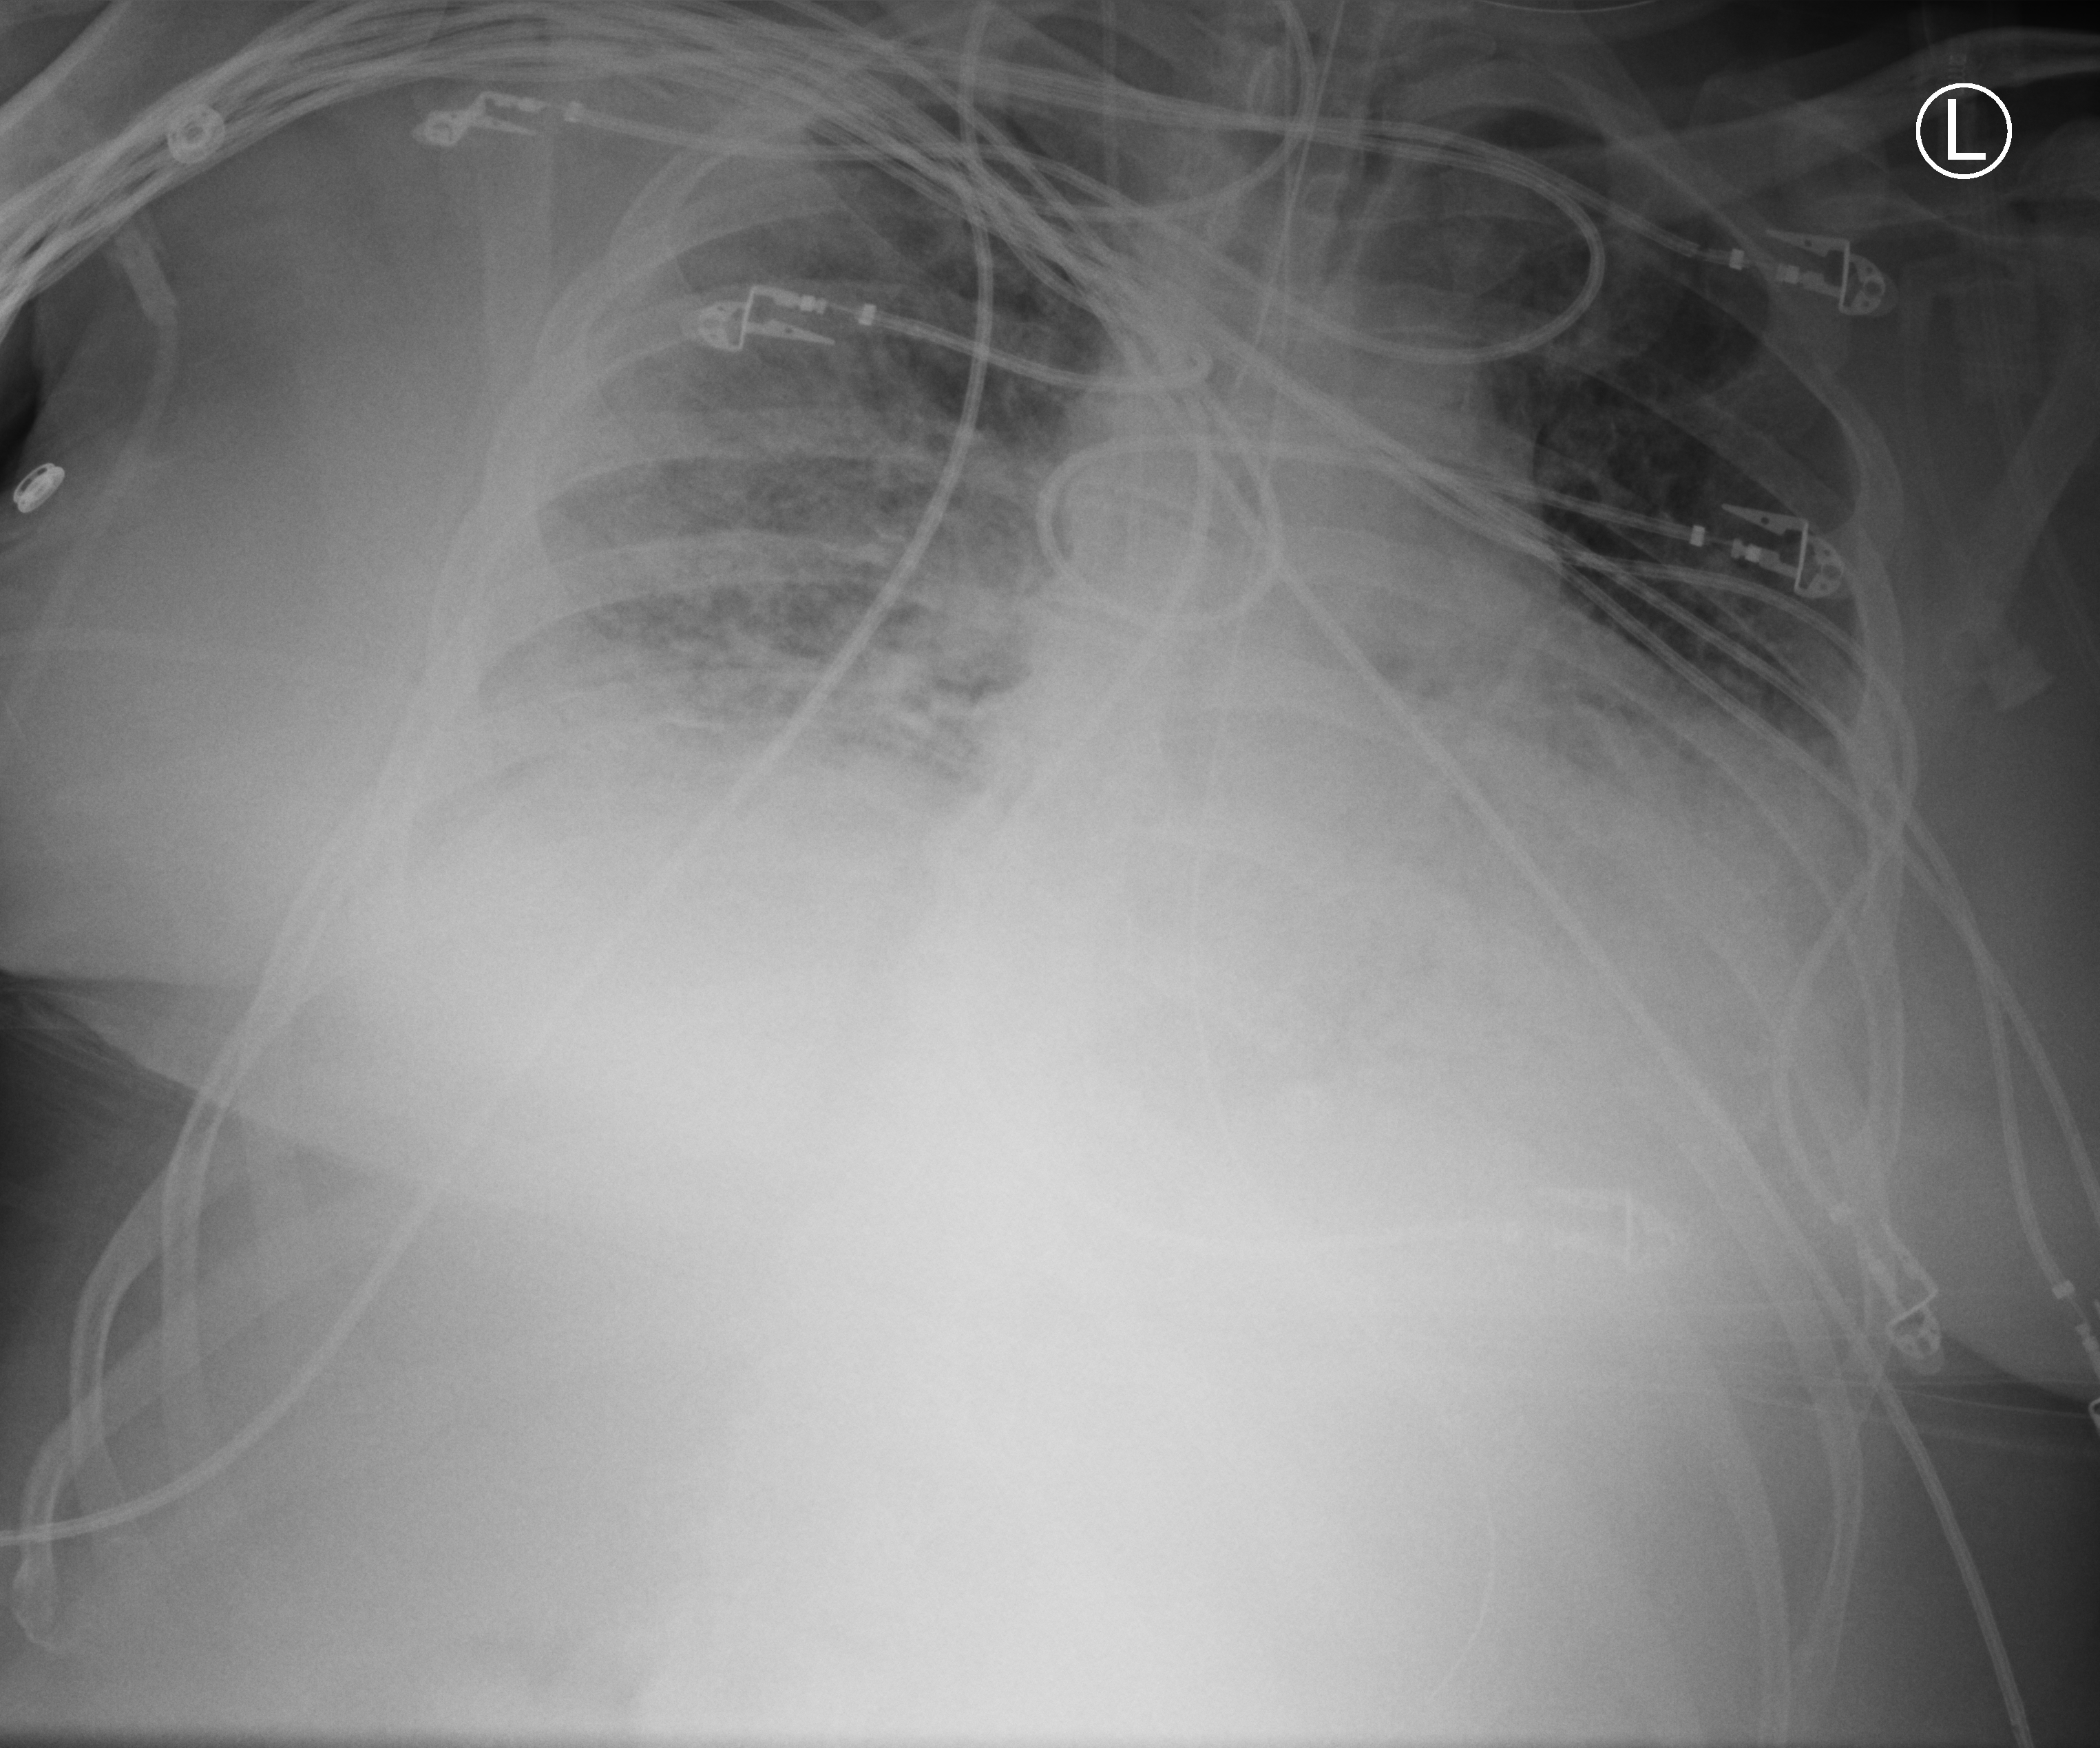
Portable chest radiograph, anteroposterior (AP) projection. Patient hospitalised with COVID-19; male, aged 60–74 years.
From the hospital-stay record, not from the radiograph (when in the stay this image was taken is not recorded): mechanically ventilated during this hospital stay: yes; length of hospital stay: 40 days.